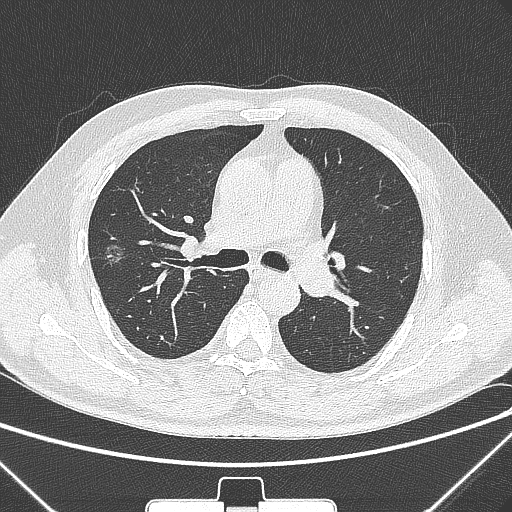
Chest CT, one axial slice; position 193 of 320 along the scan axis; 120 kVp; lung window (W 1500 / L -600 HU); 1 mm slice thickness; 512 × 512 image matrix. Male patient, age 58 years. From the clinical record (not read from this slice): clinical TNM (as recorded): T1c N0 M0.
Outlined on this slice (rectangle marked by the reading radiologist):
- lung tumour (recorded histology: adenocarcinoma): box from (x=98, y=234) to (x=134, y=282) px